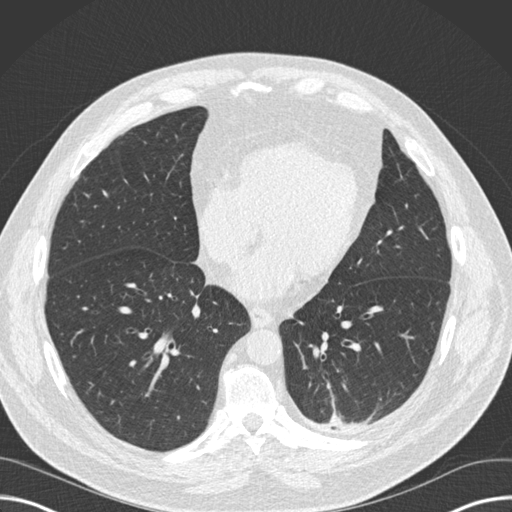
Low-dose screening chest CT, one axial slice. Position 61 of 160 along the scan axis. Reconstruction kernel B30f. 120 kVp. Lung window (W 1500 / L -600 HU). 2 mm slice thickness. 512 × 512 image matrix, field of view 382 × 382 mm.
Outlined on this slice (expert manual segmentation):
- lesion 1 (tumor, upper lobe of left lung): bounding box <330,413,355,427> (left, top, right, bottom; pixels)